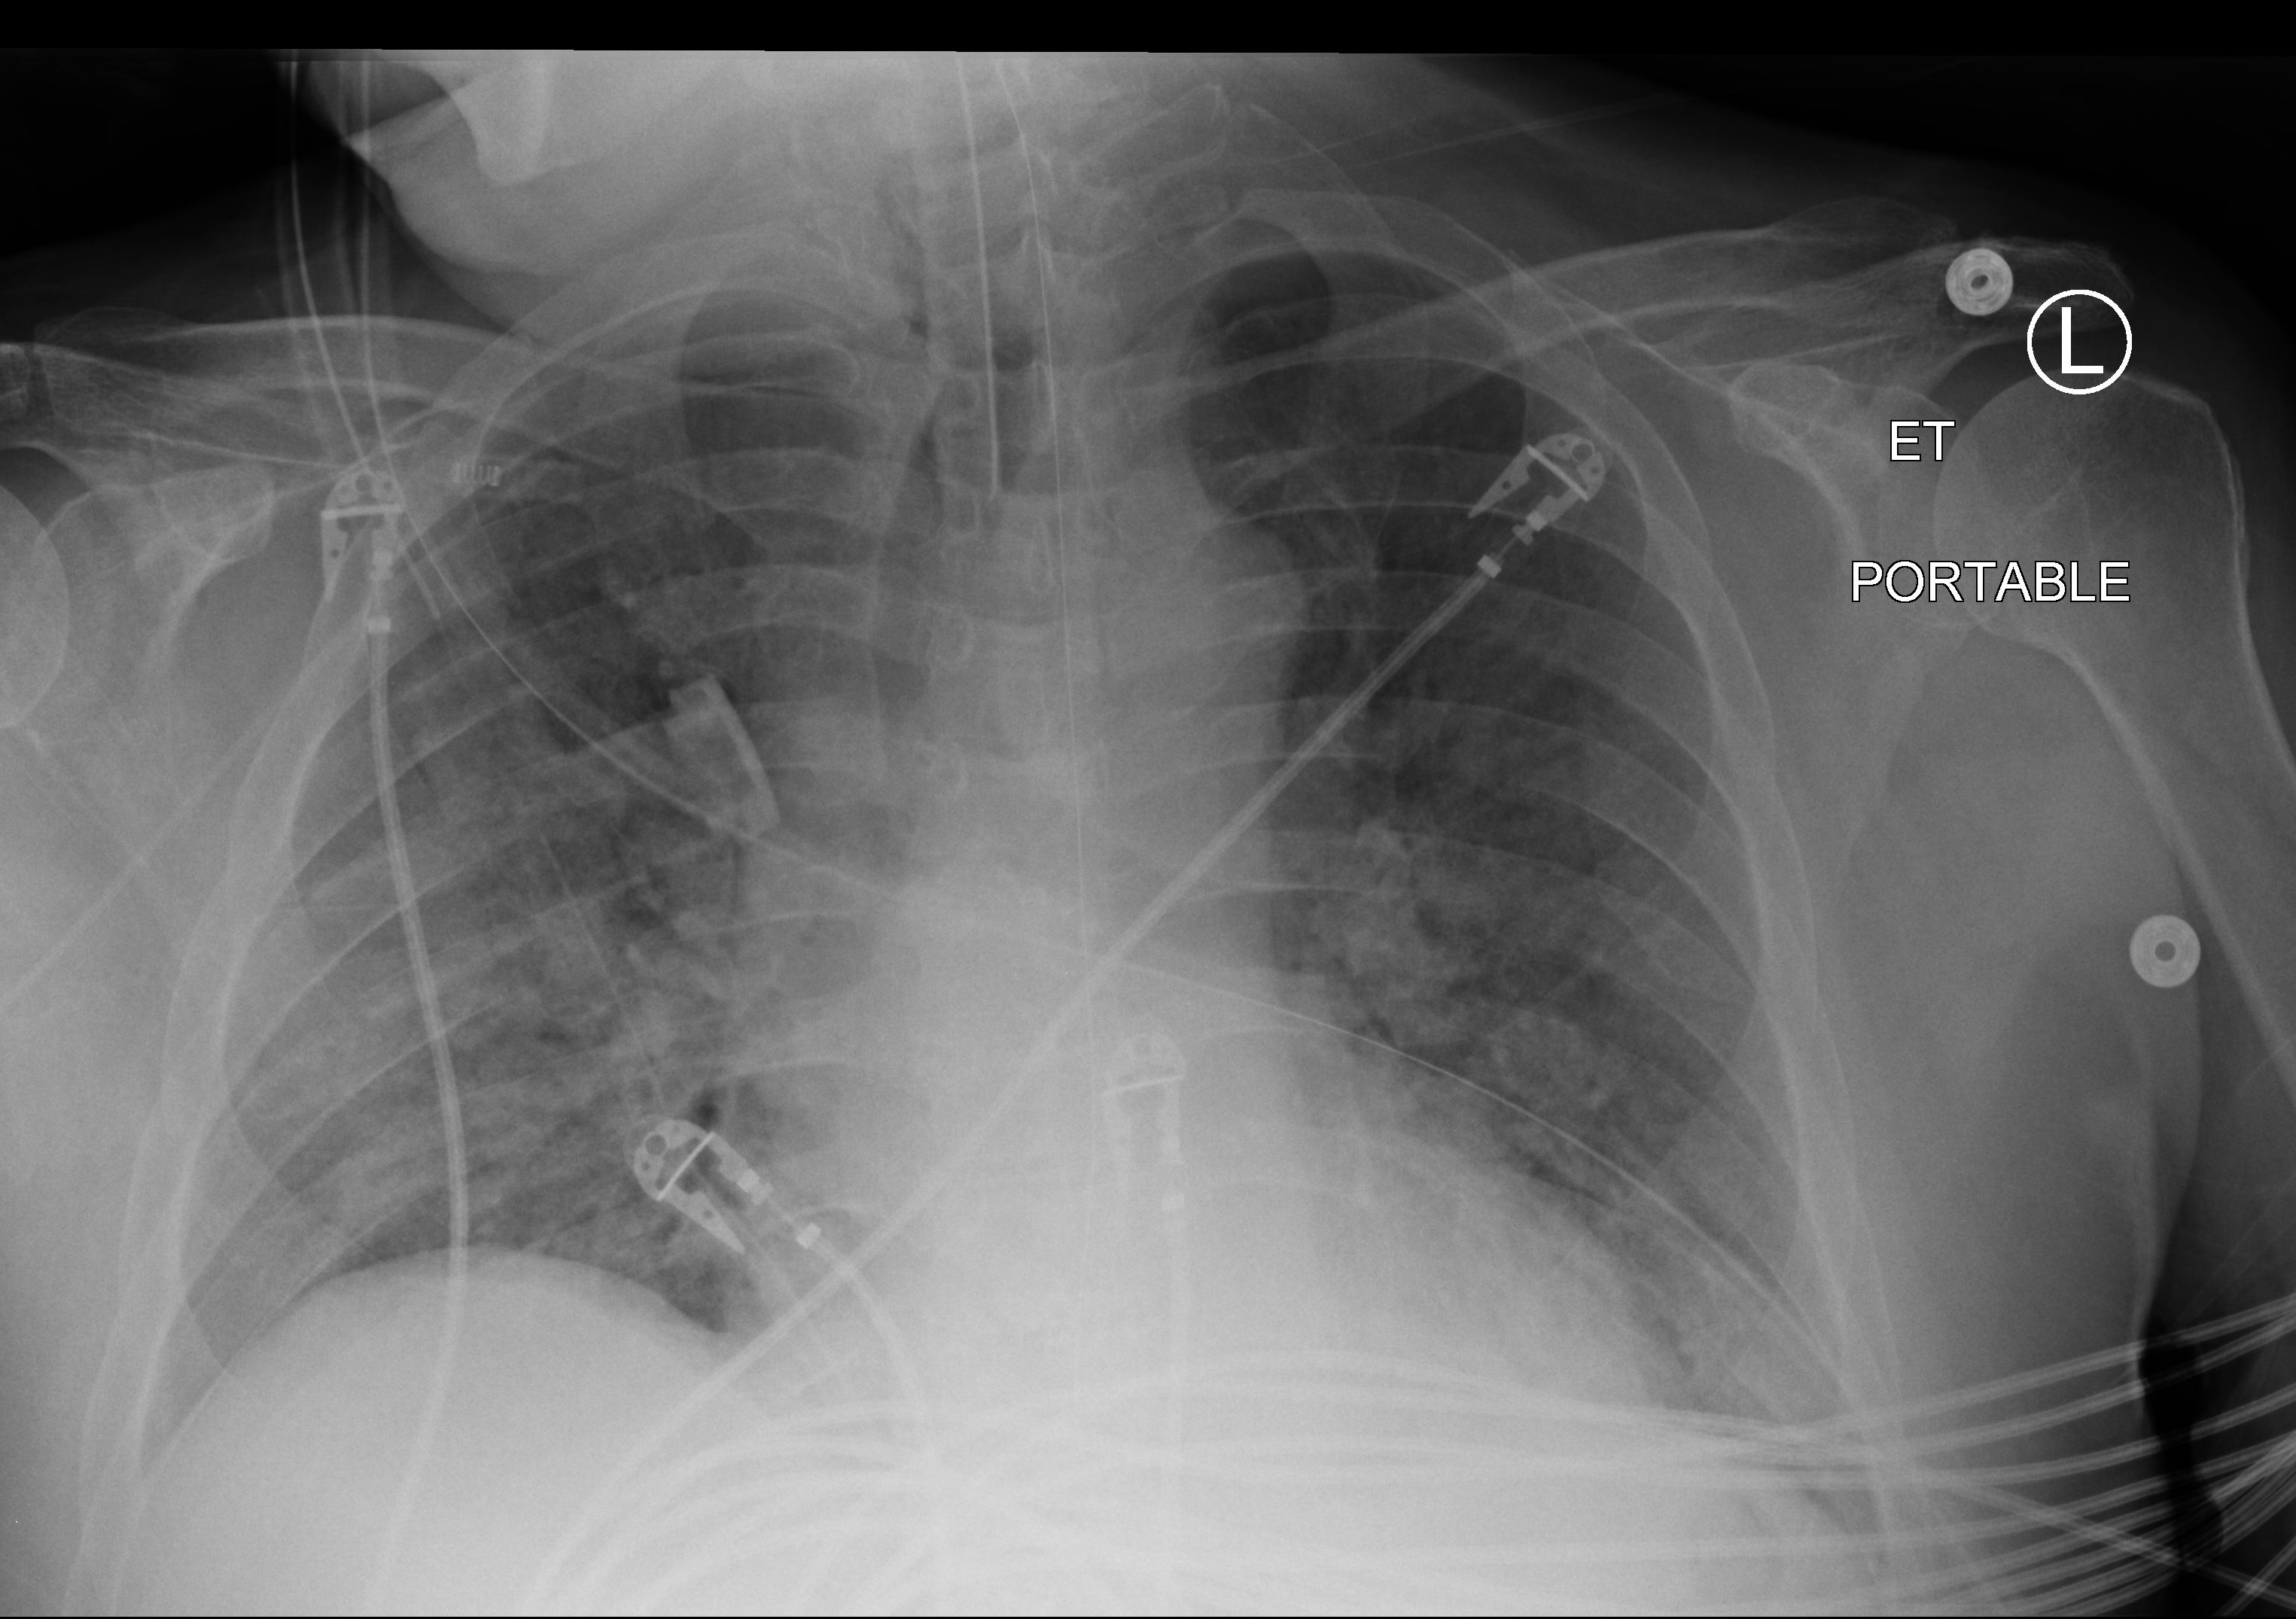
Chest X-ray (portable), anteroposterior (AP) projection. Male patient hospitalised with COVID-19, age 60–74 years.
Hospital-stay facts (about this admission, not read from this image; timing relative to this image not recorded):
- hypertension (admission record): yes